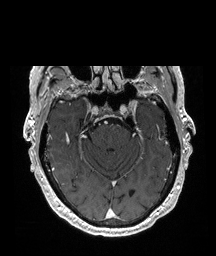
Brain MRI from a brain-tumour surgery series, one axial slice. Slice 143 of 208 in the series (ordered by position). T1-weighted post-contrast. 1 mm slice thickness. 216 × 256 image matrix, field of view 216 × 256 mm. From the clinical record (not read from this slice): histopathology: Glioblastoma; WHO grade: 4; IDH mutation: no; tumour location: Right Temporal.
Annotated regions visible in this slice (expert manual segmentation):
- tumour: box from (x=52, y=164) to (x=57, y=168) px